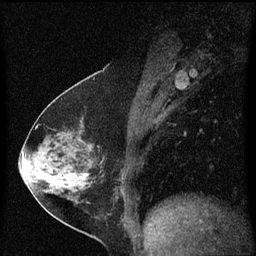
Breast MRI (dynamic contrast-enhanced), one sagittal slice. Slice 30 of 60 in the series (ordered by position). Dynamic contrast-enhanced series, image 2 of 3 at this slice position (ordered by acquisition). 1.5 T. TE 4.2 ms, TR 8.4 ms. 2 mm slice thickness. 256 × 256 image matrix, field of view 200 × 200 mm. Female patient, age 54 years. Case-level facts recorded for this patient, not image findings: setting: breast cancer imaged before/during neoadjuvant chemotherapy; receptor status: HER2-positive.
Structures marked on this image (semi-automatic segmentation, software-assisted and operator-edited):
- analysis volume of interest (the breast-tissue region the enhancement analysis was run in; not a lesion): box from (x=32, y=122) to (x=121, y=213) px
- tumour enhancement mask (voxels above the 70 % enhancement threshold inside the analysis volume of interest): (x=78, y=174)–(x=89, y=179)